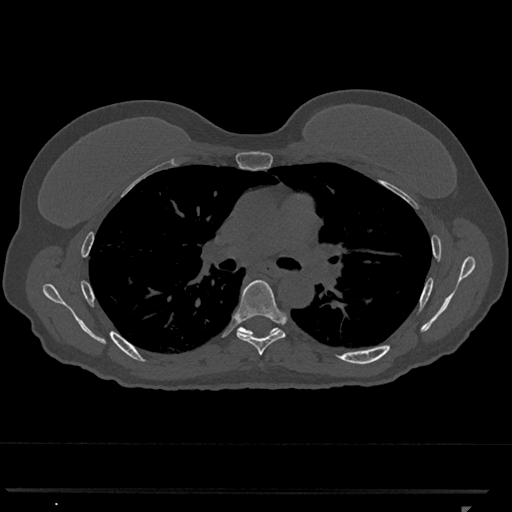
CT including the spine, one axial slice; position 753 of 793 along the scan axis; 120 kVp; bone window (W 1800 / L 400 HU); 512 × 512 image matrix, field of view 380 × 380 mm. Patient: female, 62 years. Case-level facts recorded for this patient, not image findings: primary cancer: renal.
Annotated regions visible in this slice (semi-automatic segmentation, software-assisted and operator-edited):
- T6 vertebra: box from (x=236, y=279) to (x=285, y=356) px
- T7 vertebra: (x=237, y=327)–(x=278, y=336)